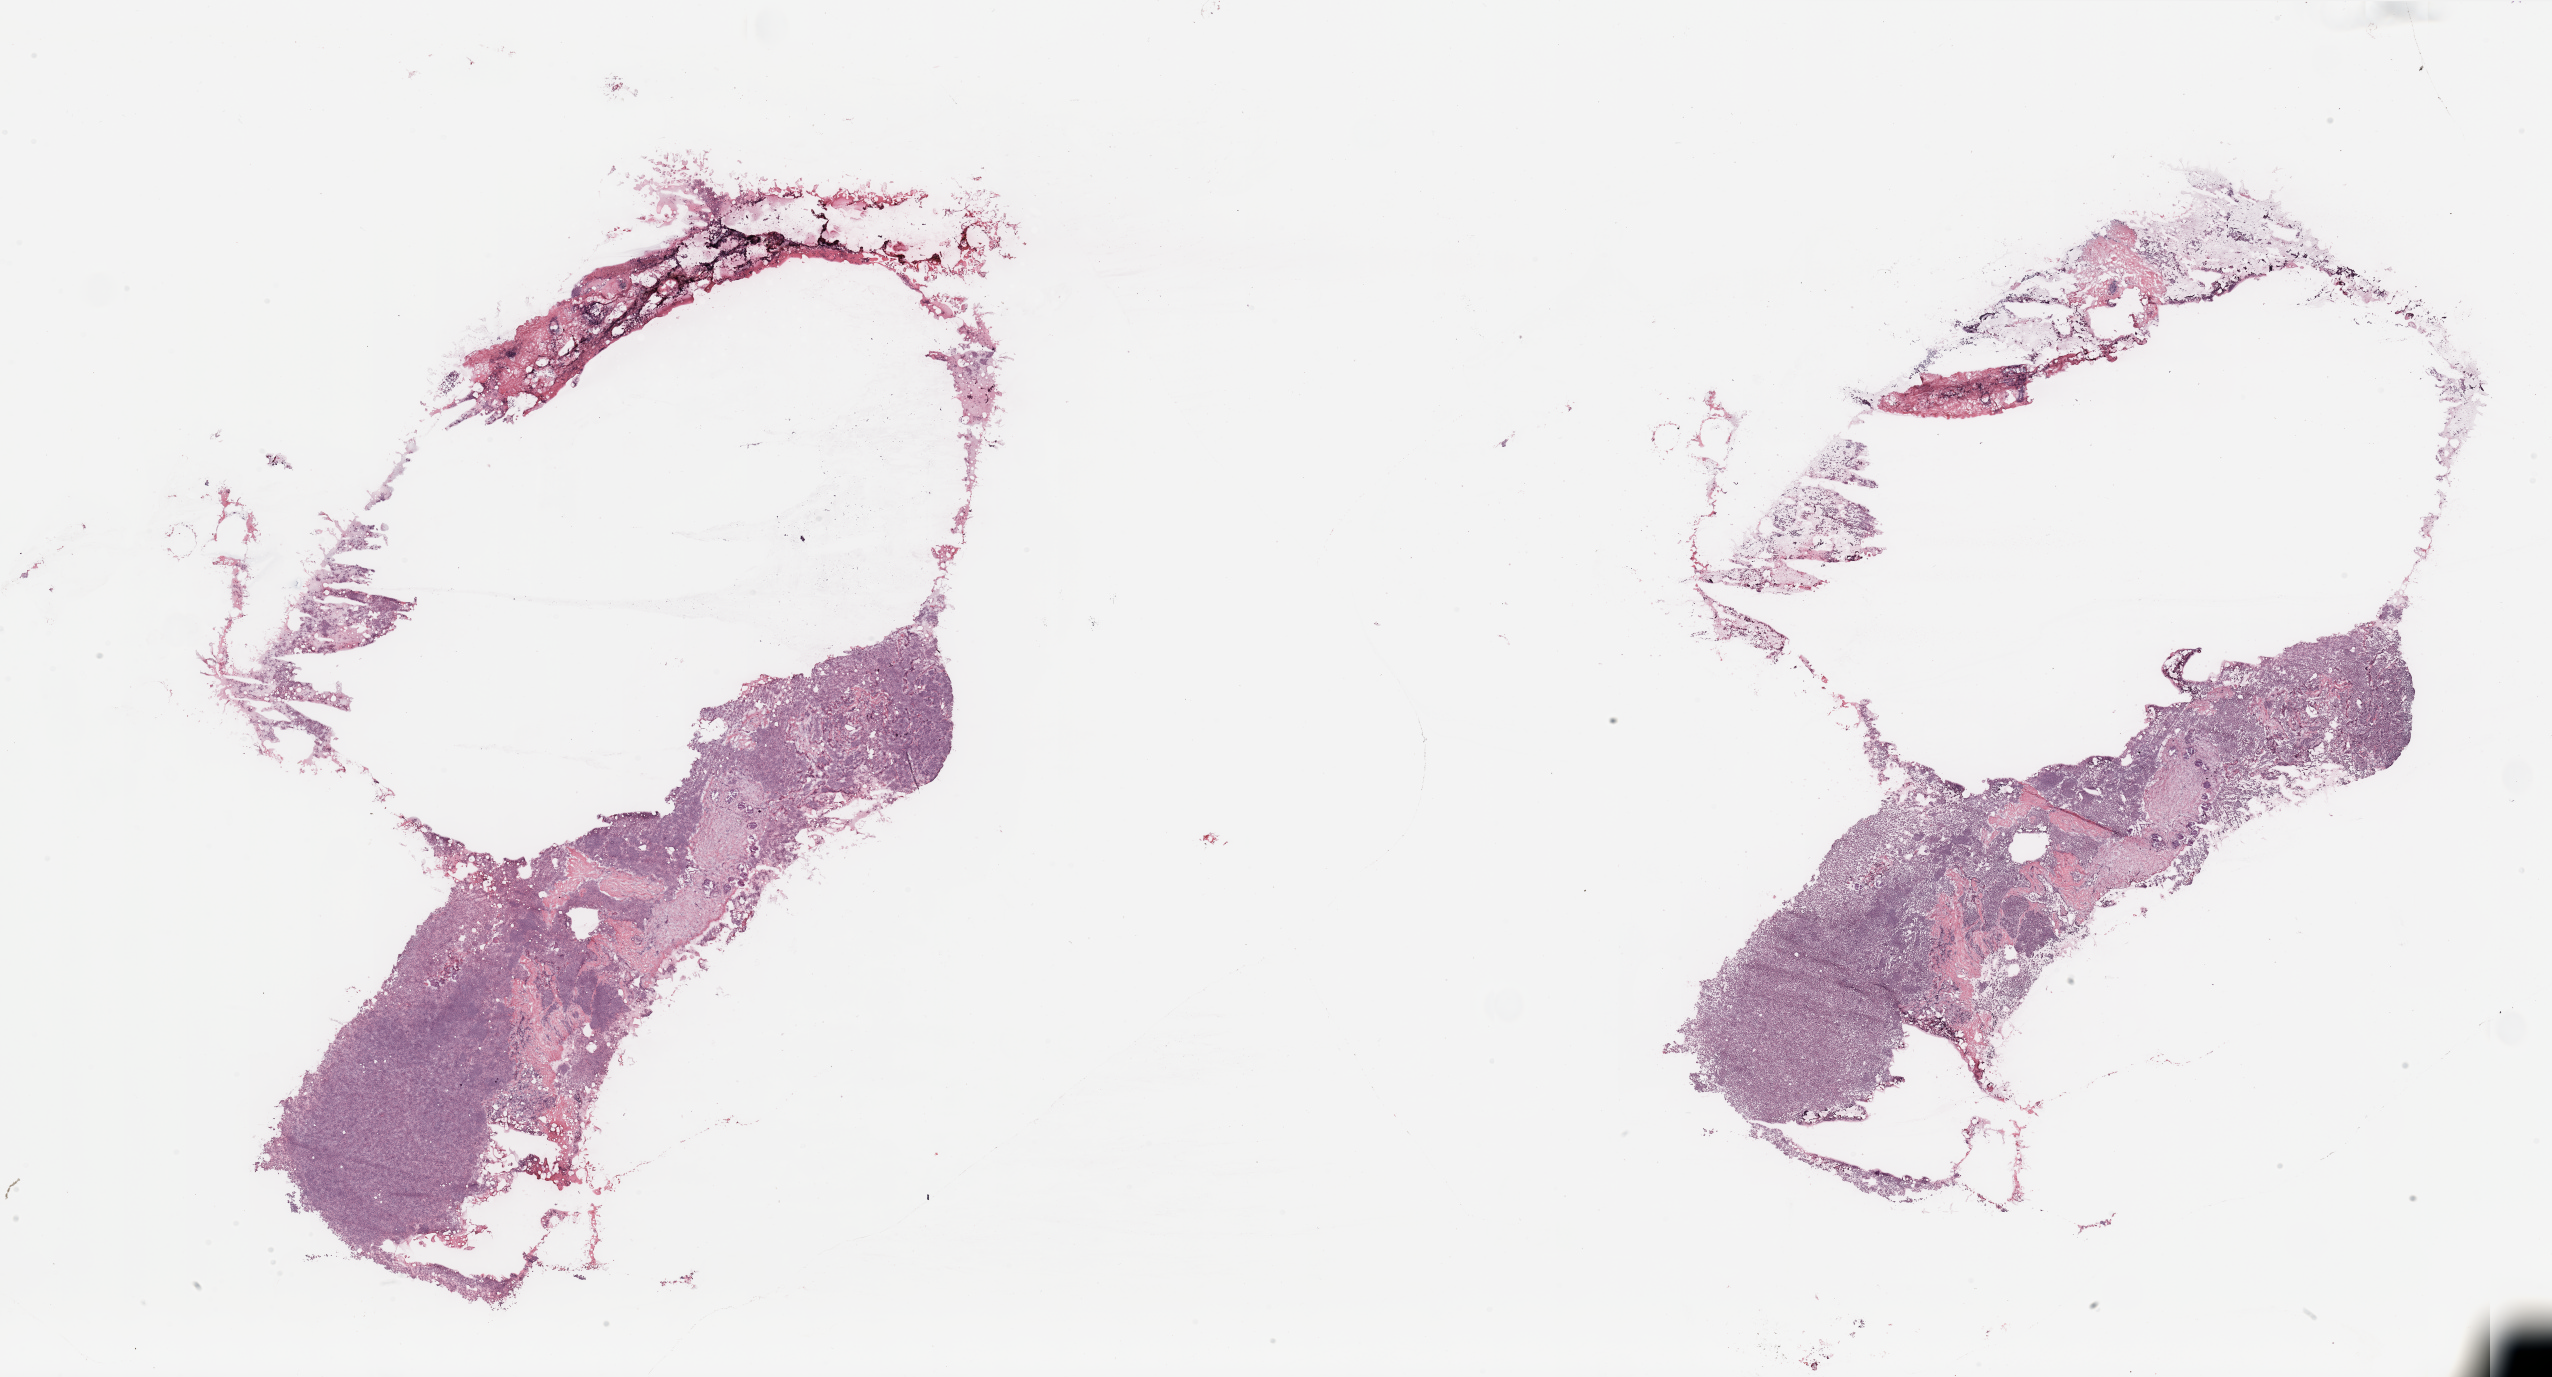
Whole-slide histology image, Hematoxylin and eosin (H&E) stained, whole scanned area (about 40.4 x 21.8 mm) shown as a low-resolution overview, breast, tissue type not recorded.
Patient diagnosis (cohort enrolment): breast cancer (breast).